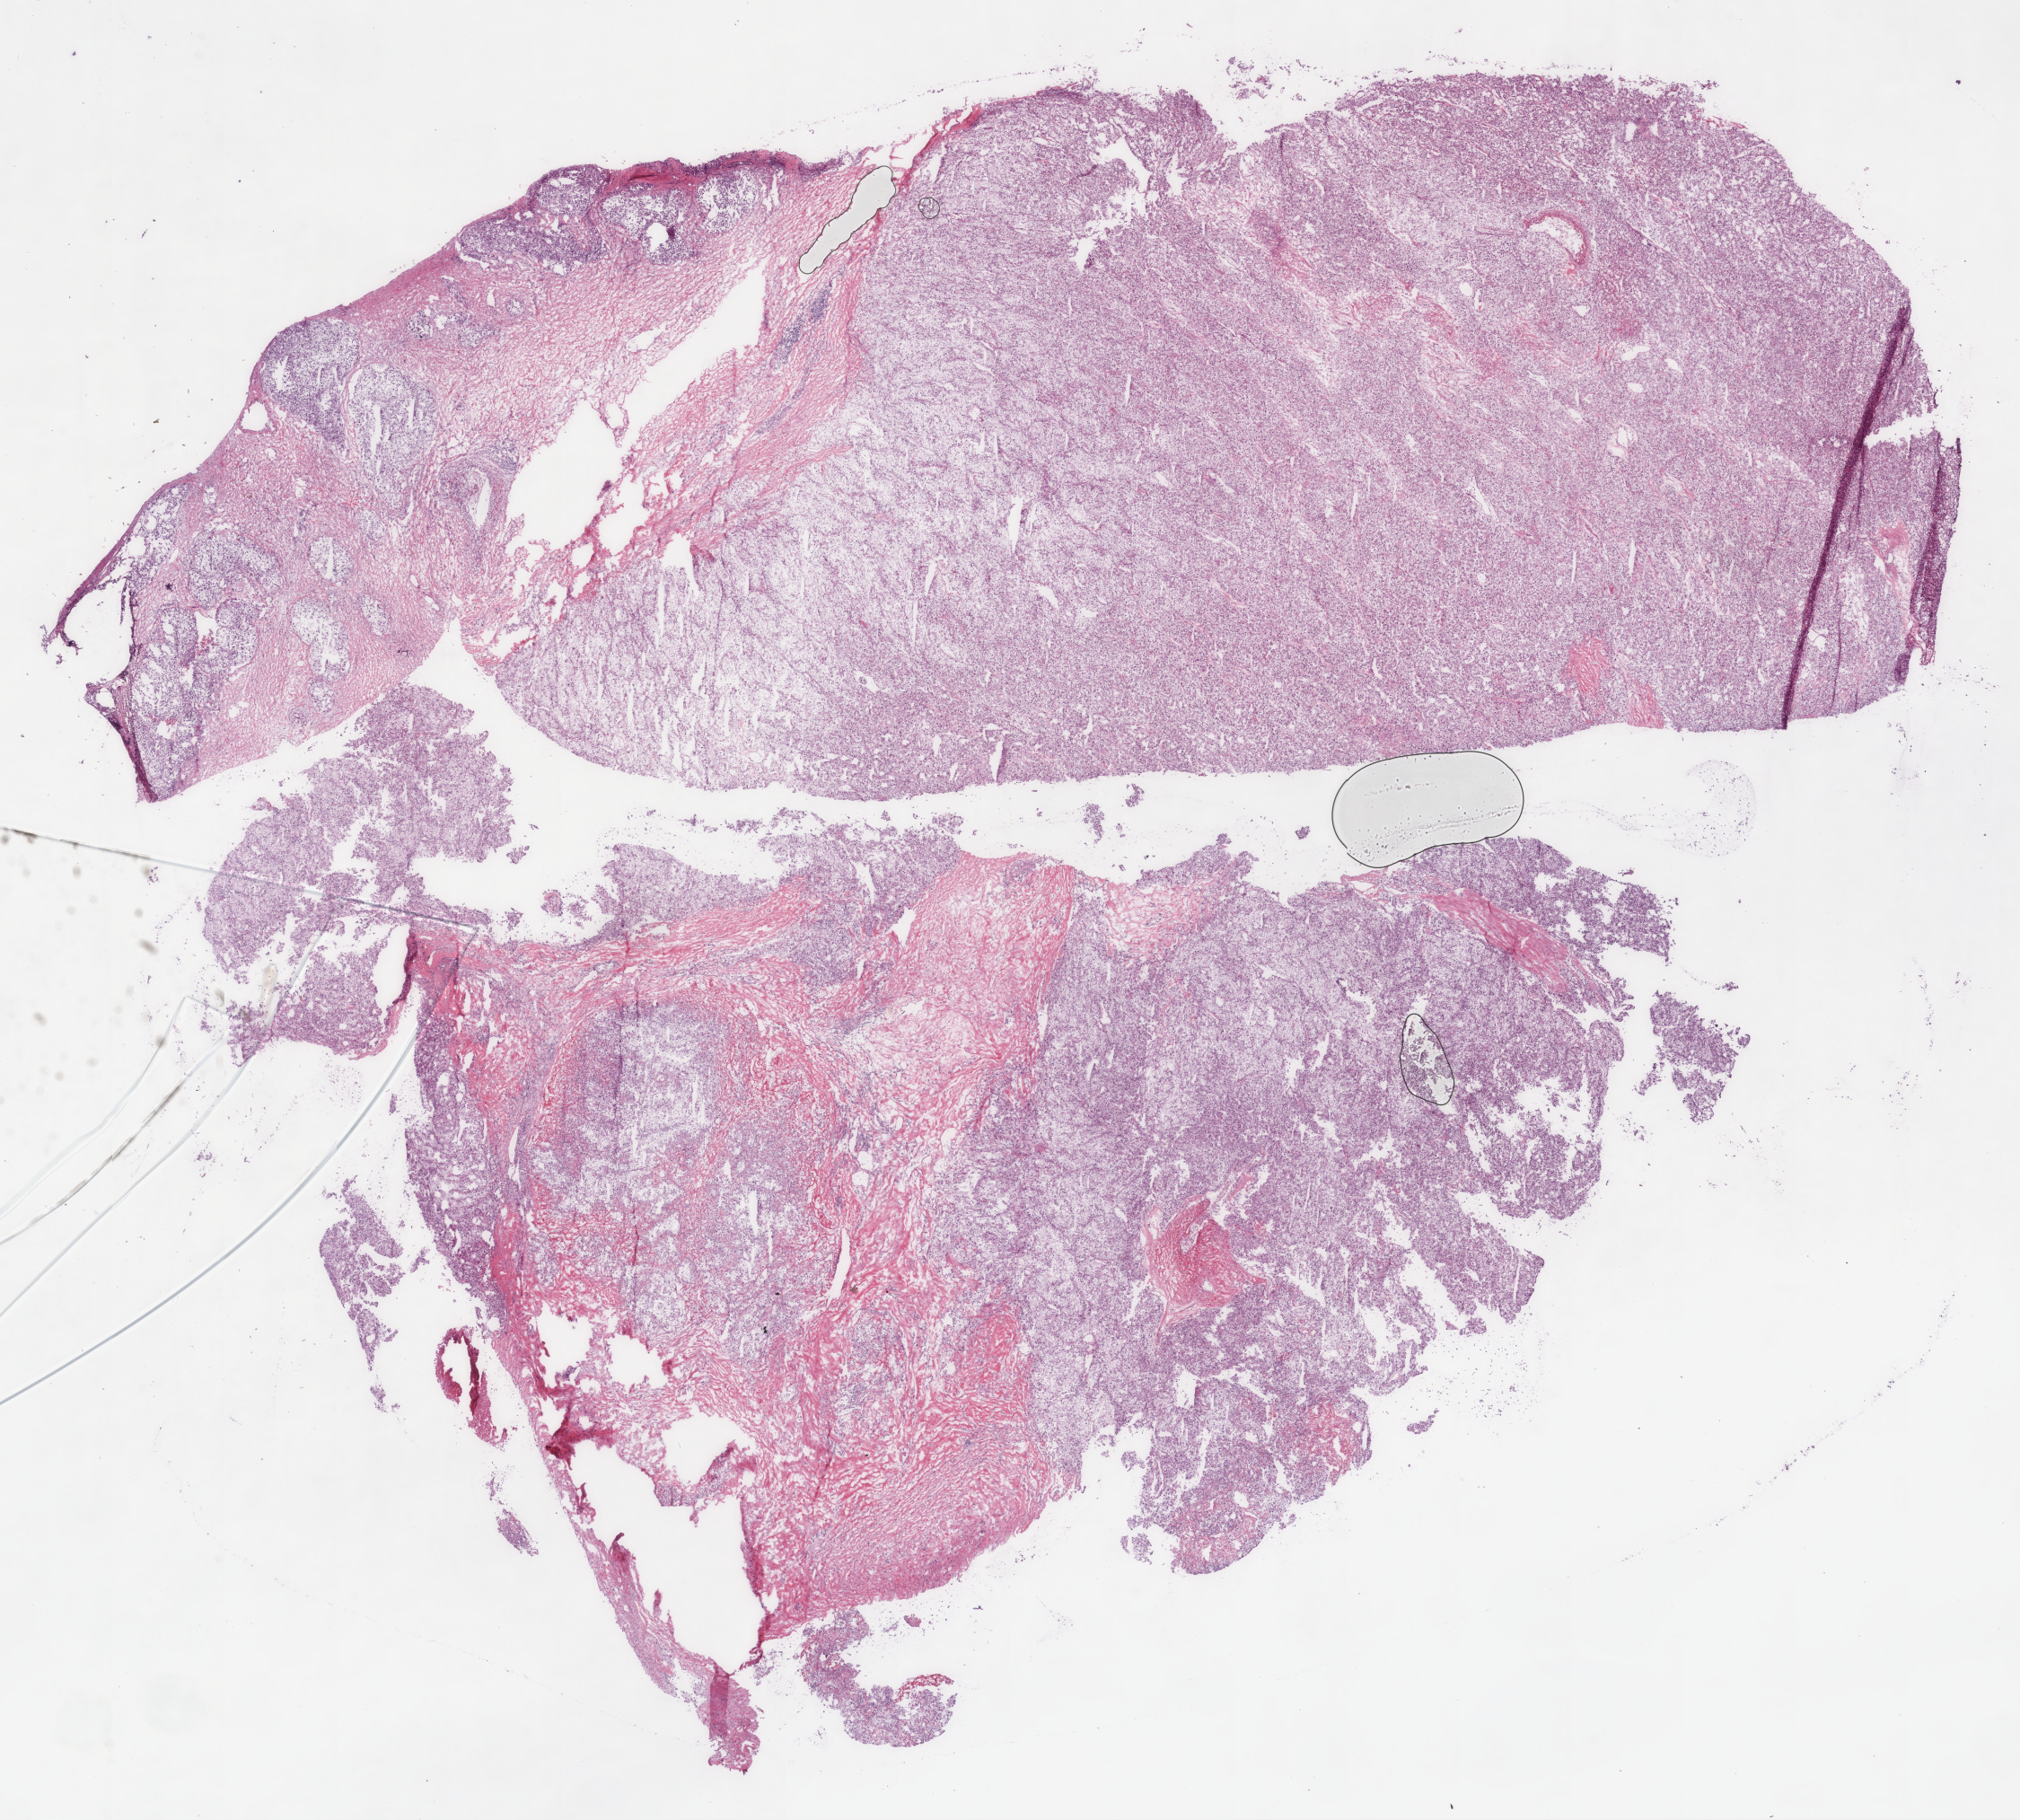
Whole-slide histology image, H&E-stained, low-resolution overview of the scanned area, about 18.1 x 16.3 mm (acquisition: 20x scan). Frozen section. Kidney, primary tumour sample. Male patient; age at initial diagnosis 60 years. Pathologist review of this section (percent, as recorded): tumour cells 75%, tumour nuclei 80%.
Histologic diagnosis: Clear cell adenocarcinoma, NOS.